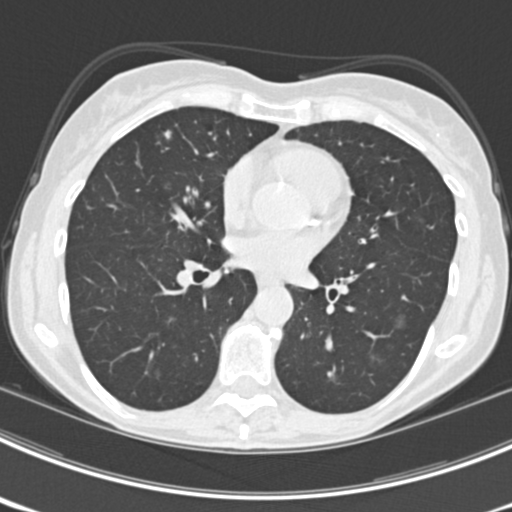
Chest CT (low-dose screening protocol), one axial image, third screening round (two years after baseline), lung window (W 1500 / L -600 HU), 2 mm slice thickness, standard (soft-tissue) reconstruction kernel (B30f). Female, age 63 years at enrolment.
Lesion marked by an expert reader, bounding box [x1, y1, x2, y2] px = [405, 200, 446, 236]. The screening reader recorded 9 non-calcified nodules or masses ≥4 mm on this exam (left upper lobe, right upper lobe, left upper lobe, left lower lobe, right middle lobe, left lower lobe, left lower lobe, right lower lobe, right lower lobe); which of them this box marks is not recorded.